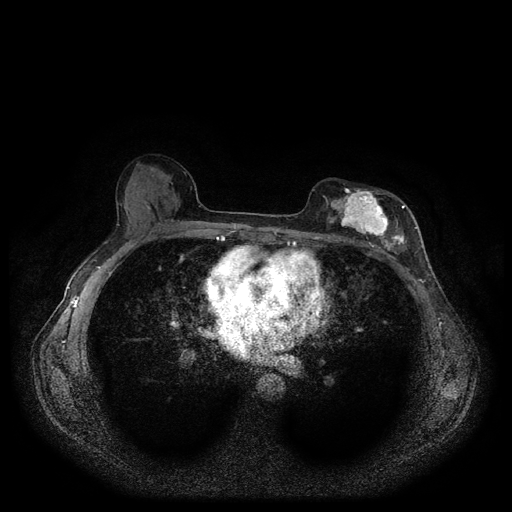
Breast MRI (dynamic contrast-enhanced, multi-phase), one axial slice. Slice 57 of 116 in the series (ordered by position). Dynamic contrast-enhanced series, time point 2 of 5 at this slice position (early post-contrast). 1.5 T. TE 2.6 ms, TR 5.3 ms. 512 × 512 image matrix, field of view 350 × 350 mm. Female patient, age 51 years.
Outlined on this slice (semi-automatically segmented with operator editing):
- breast lesion (labelled 'tumour' in the annotation; benign lesions carry a separate 'benign' label): bounding box (x1, y1, x2, y2) in pixels: (325, 183, 410, 255)